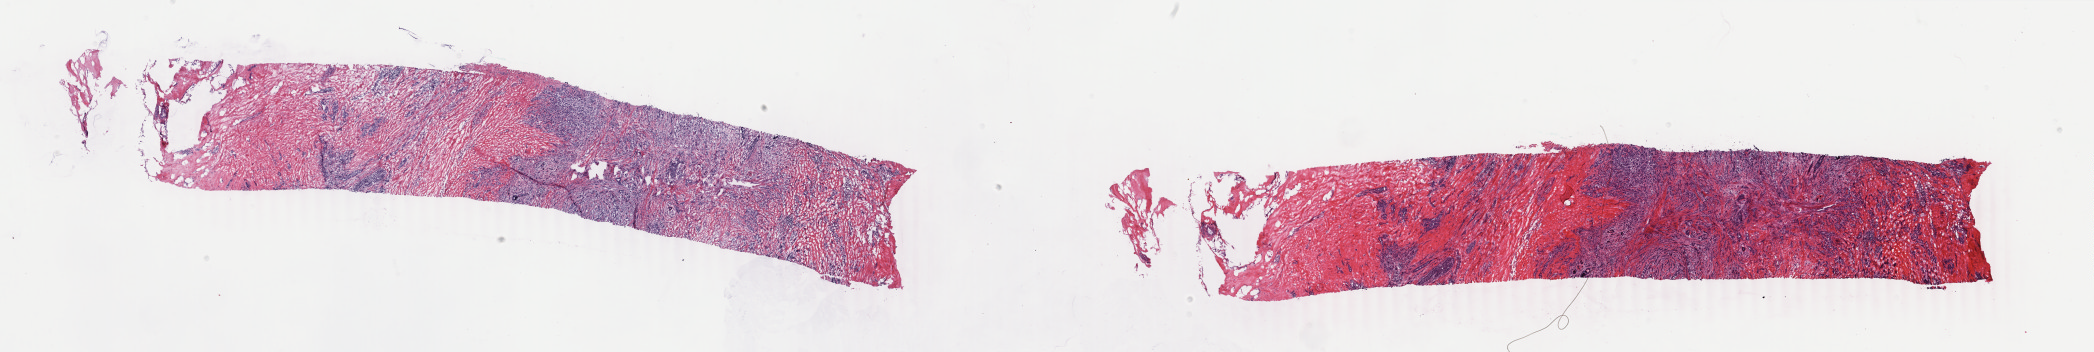
Whole-slide histology image, H&E-stained, shown as a low-resolution overview of the whole scanned area (about 33.3 x 5.6 mm, acquisition: 40x scan), frozen section, sample: primary tumour, breast. Female patient; age at initial diagnosis 46 years. Composition of this section per pathologist review: tumour cells 50%, tumour nuclei 70%, normal cells 39%, stromal cells 10%, necrosis 1%. Inflammatory infiltration, as recorded: lymphocyte infiltration 10%, monocyte infiltration 0%, neutrophil infiltration 0%.
* pathologic diagnosis: Lobular carcinoma, NOS
* AJCC pathologic stage: IIB (6th edition)
* lymph nodes positive (case pathology): 0 of 1 examined
* laterality: left